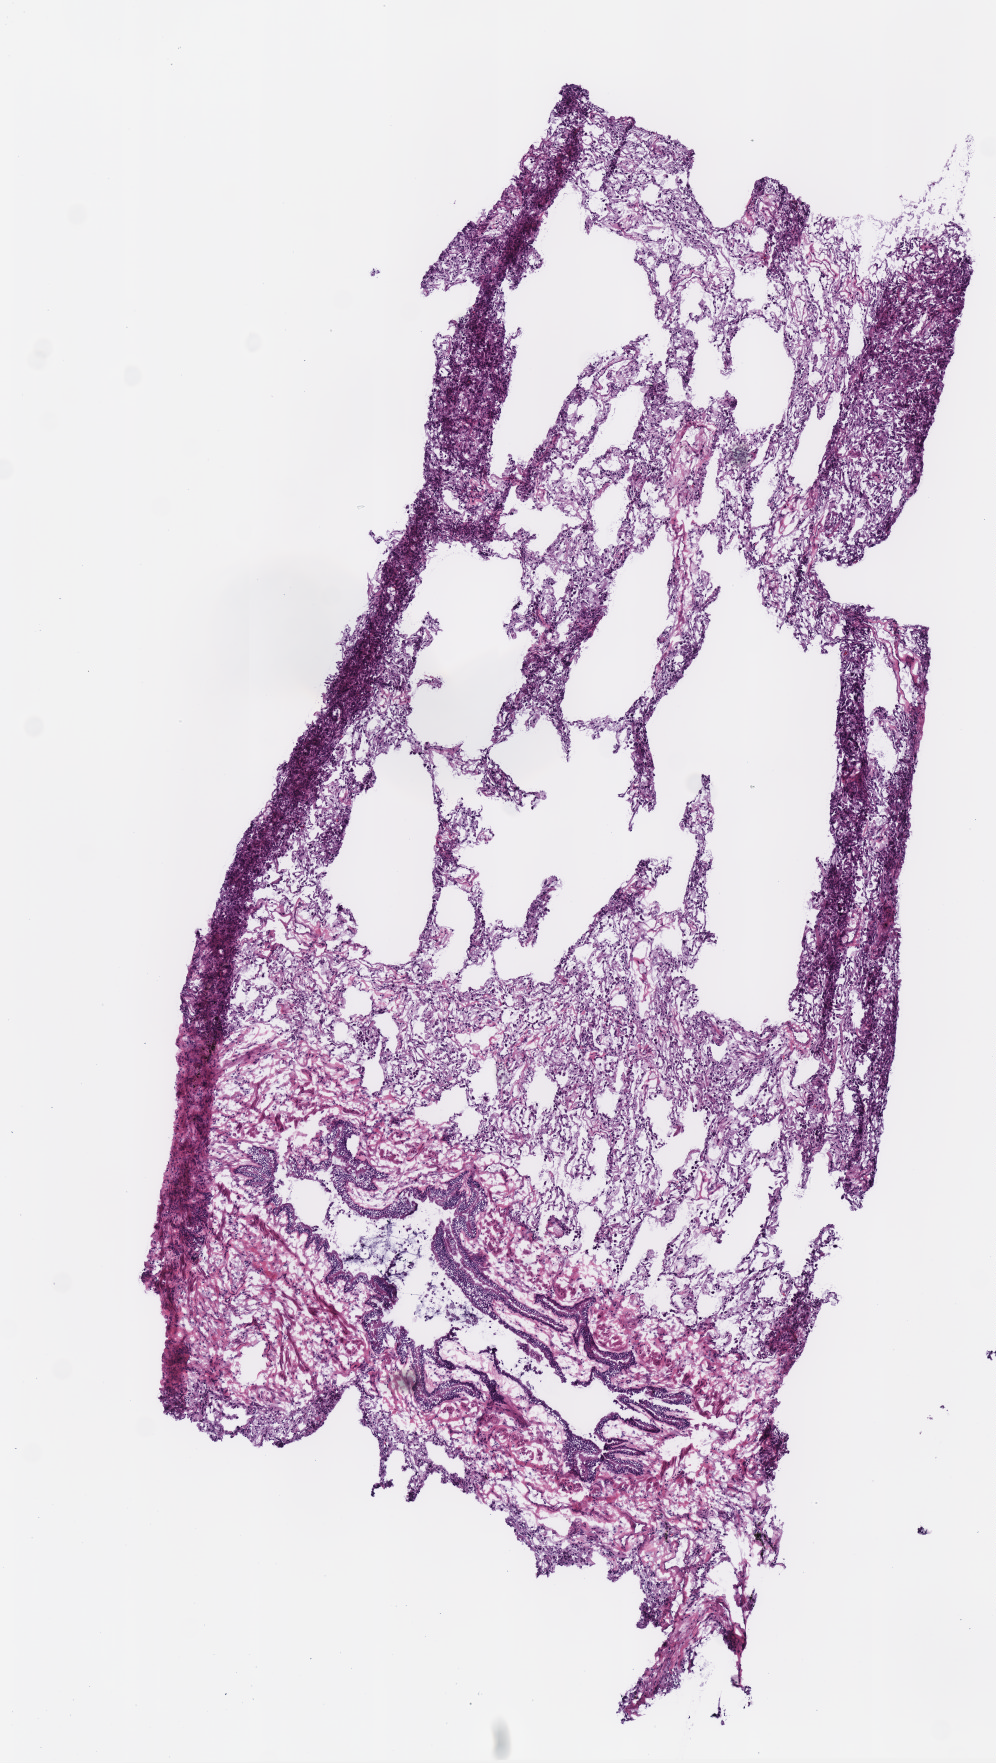
Digitized H&E tissue section (whole slide) — a low-resolution overview of the entire scanned area, about 3.9 x 6.9 mm. Frozen section from the top of the tissue portion. Solid tissue normal (non-tumour tissue) sample from the lung. Male patient; age at initial diagnosis 62 years.
This section: solid tissue normal (non-tumour) sample from the same patient. Patient diagnosis: Adenocarcinoma, NOS (lower lobe, lung).